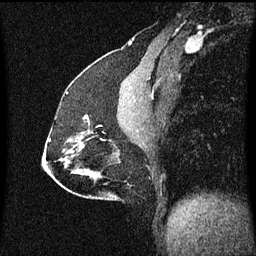
Breast MRI (dynamic contrast-enhanced), one sagittal slice; position 29 of 60 along the scan axis; dynamic contrast-enhanced series, image 2 of 3 at this slice position (ordered by acquisition); 1.5 T; TE 4.2 ms, TR 8.4 ms; 2 mm slice thickness; 256 × 256 image matrix. Patient: female, 51 years.
Structures marked on this image (semi-automatically segmented with operator editing):
- analysis volume of interest (the breast-tissue region the enhancement analysis was run in; not a lesion): bounding box (x1, y1, x2, y2) in pixels: (80, 116, 107, 139)
- tumour enhancement mask (voxels above the 70 % enhancement threshold inside the analysis volume of interest): (85, 116, 88, 121)